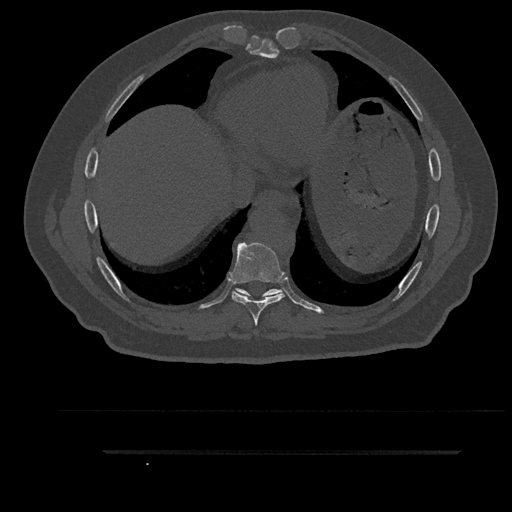
CT including the spine, one axial slice; slice 460 of 797 in the series (ordered by position); reconstruction kernel Br40s/3; 120 kVp; bone window (W 1800 / L 400 HU); 512 × 512 image matrix, field of view 432 × 432 mm. Male patient, age 63 years. From the clinical record (not read from this slice): primary cancer: renal.
Annotated regions visible in this slice (semi-automatic segmentation, software-assisted and operator-edited):
- T8 vertebra: bounding box (x1, y1, x2, y2) in pixels: (231, 242, 285, 325)
- T9 vertebra: (235, 288, 282, 299)